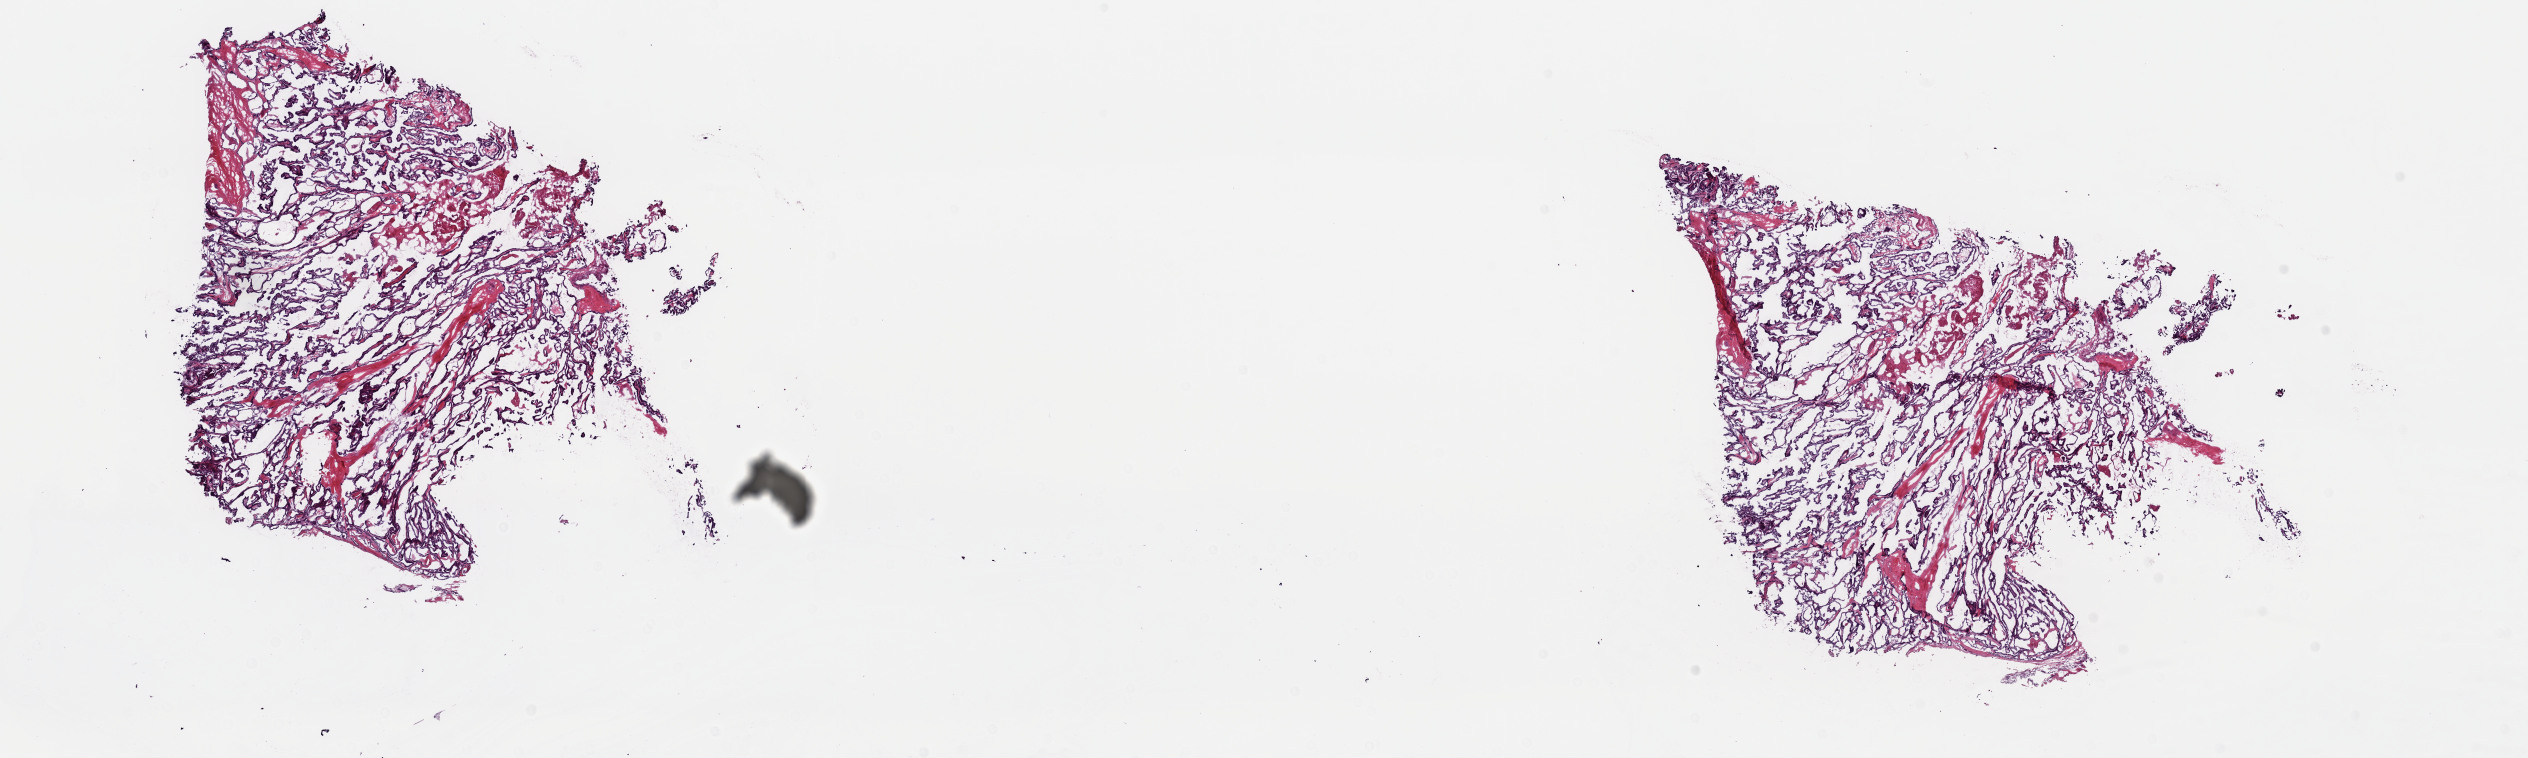
H&E whole-slide image — whole scanned area (about 20.0 x 6.0 mm, from a 40x scan) shown as a low-resolution overview. Frozen section from the top of the tissue portion. Thyroid, primary tumour sample. Patient: female, age at initial diagnosis 51 years. Pathologist review of this section (percent, as recorded): tumour cells 60%, tumour nuclei 100%, normal cells 0%, stromal cells 40%, necrosis 0%. Inflammatory infiltration, as recorded: lymphocyte infiltration 0%, monocyte infiltration 0%, neutrophil infiltration 0%.
AJCC pathologic stage: II (7th edition). Pathologic diagnosis: Papillary adenocarcinoma, NOS (thyroid gland).